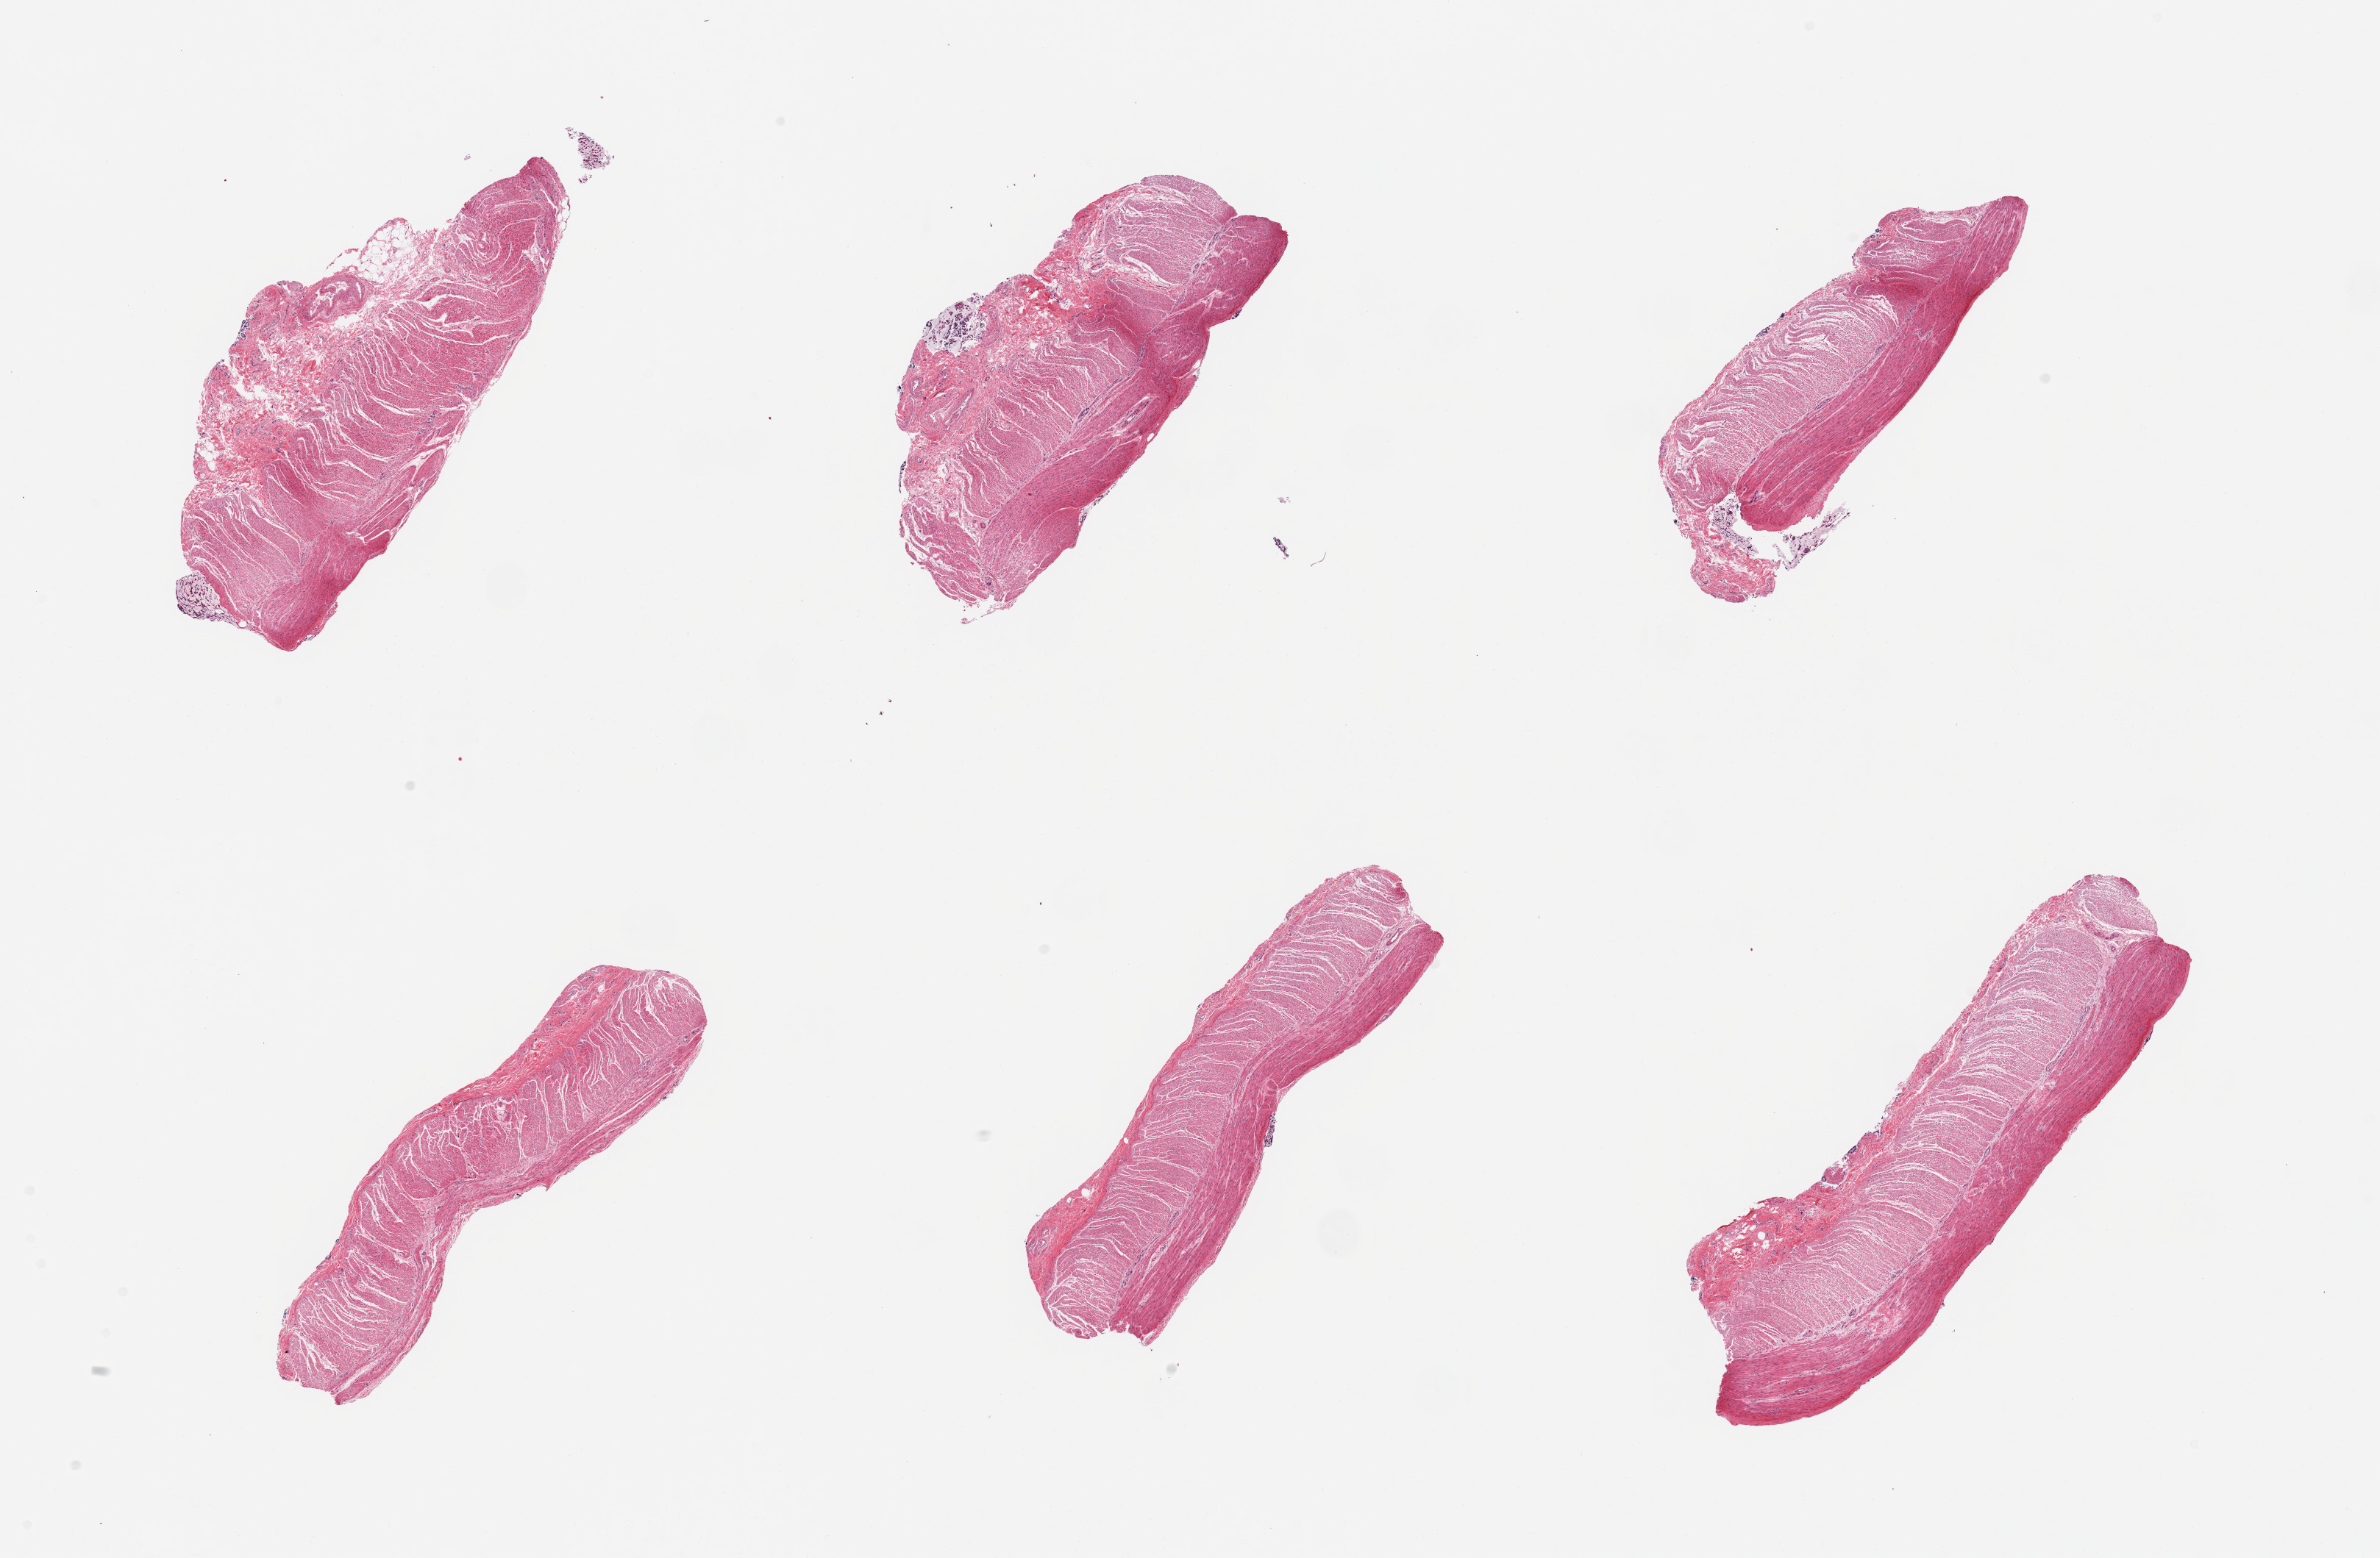
Digitized hematoxylin and eosin (H&E)-stained section, low-resolution overview of the scanned area, about 25.6 x 16.8 mm (slide scanned at 20x). PAXgene-fixed paraffin-embedded (PFPE) section. Sampled site (target tissue): sigmoid colon. Tissue donor sample. Donor: male.
- pathologist's review note for this sample: 6 pieces, essentially all muscularis, minut focus of completely autolyzed mucosa